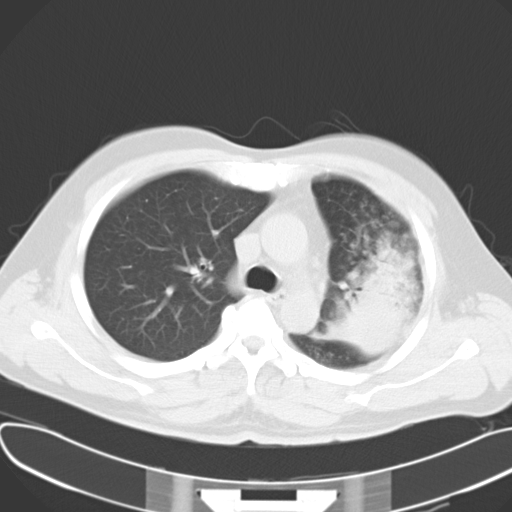
Chest CT, one axial slice; position 22 of 30 along the scan axis; reconstruction kernel B40f; 120 kVp; lung window (W 1500 / L -600 HU); 10 mm slice thickness; 512 × 512 image matrix, field of view 377 × 377 mm. Male patient, age 48 years. Case-level facts recorded for this patient, not image findings: clinical TNM (as recorded): T4 N0 M0.
Structures marked on this image (rectangle marked by the reading radiologist):
- lung tumour (recorded histology: adenocarcinoma): bounding box <325,252,416,360> (left, top, right, bottom; pixels)